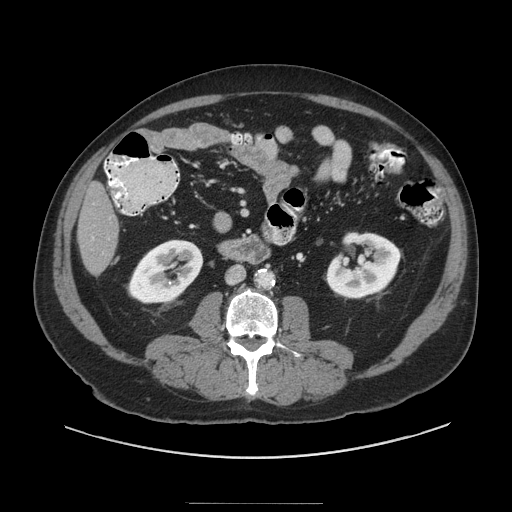
Contrast-enhanced abdominal CT (liver protocol), one axial slice; slice 21 of 91 in the series (ordered by position); soft-tissue window (W 400 / L 40 HU); 2.5 mm slice thickness; 512 × 512 image matrix, field of view 440 × 440 mm. From the clinical record (not read from this slice): diagnosis: hepatocellular carcinoma (patient treated with transarterial chemoembolisation; whether this scan precedes or follows treatment is not stated here); TNM stage (as recorded): Stage-I; Child-Pugh class: A; tumour differentiation: well differentiated; tumour nodularity: uninodular.
Structures marked on this image (semi-automatic segmentation, software-assisted and operator-edited):
- liver parenchyma outside the tumour (the mass and vessels are separate outlines, so this box may not span the whole liver): box from (x=78, y=182) to (x=118, y=274) px